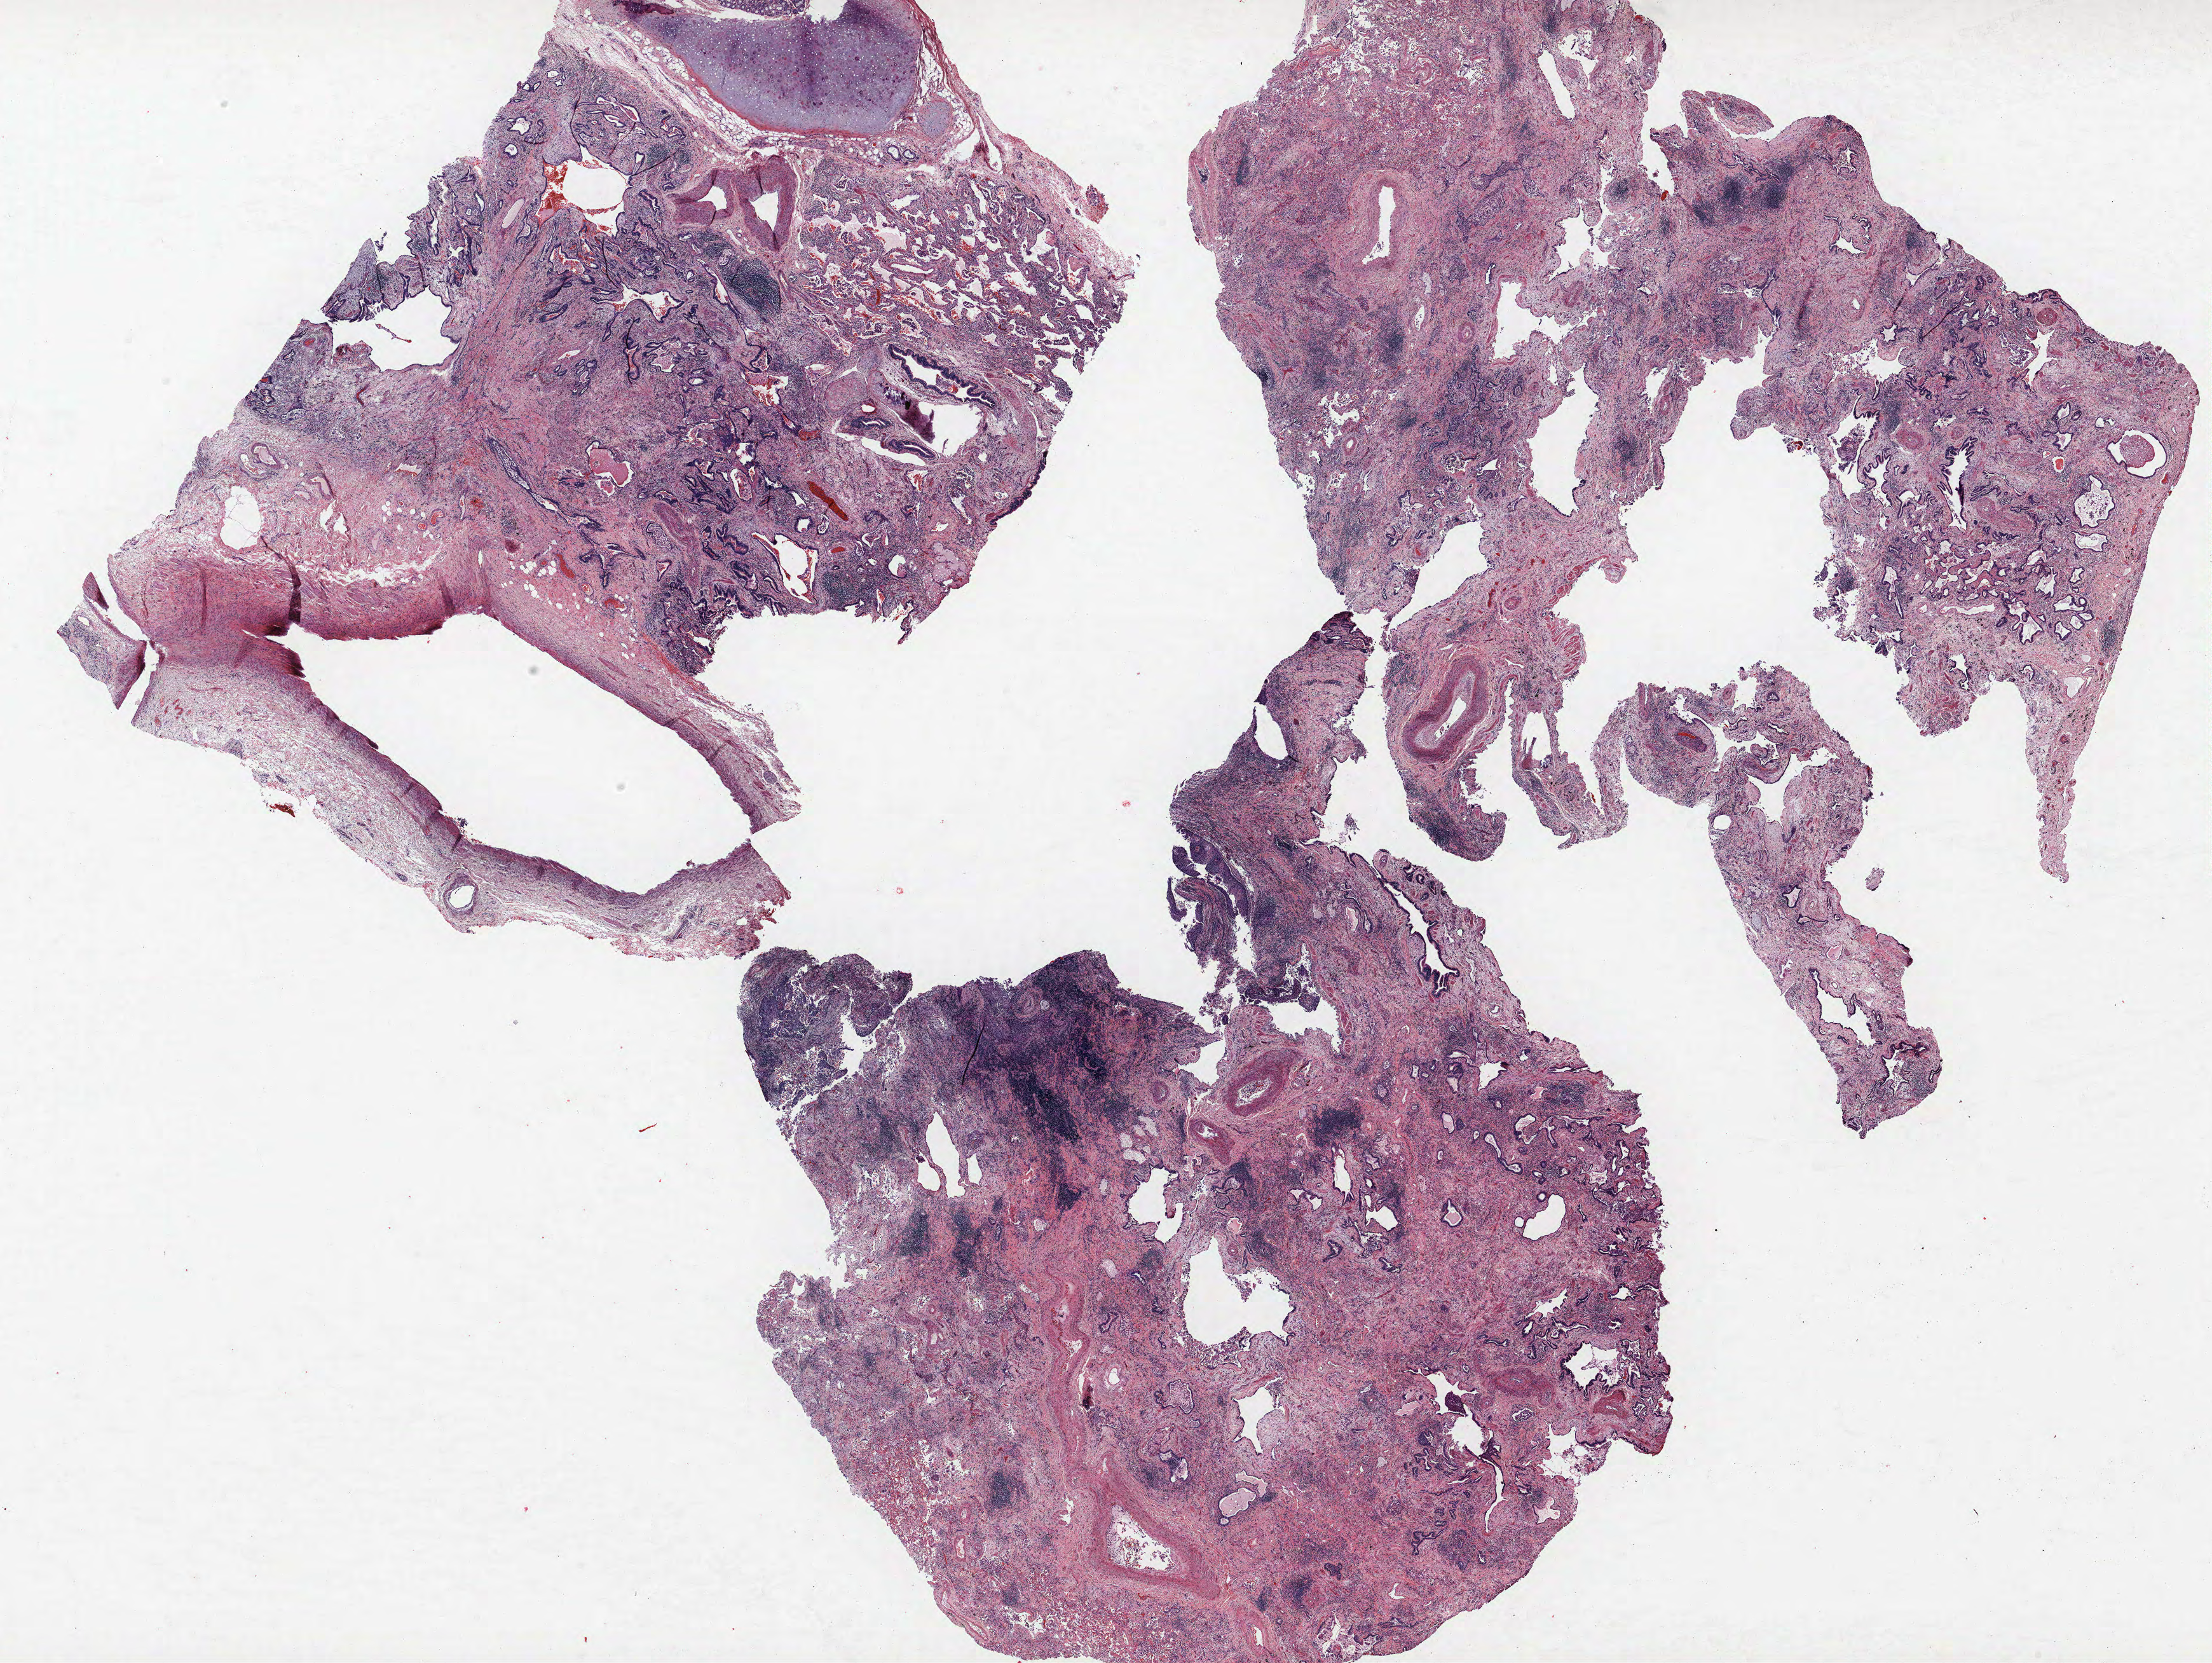
Whole-slide histology image, H&E-stained, shown as a low-resolution overview of the whole scanned area (about 27.8 x 20.9 mm, from a 40x scan); FFPE section; lung tissue. Male, age 68 at enrolment. Grade: well differentiated (G1).
* primary tumour location (clinical record): left upper lobe
* tumour size (pathology): 17 mm
* stage (AJCC 6th edition): IA
* participant's lung-cancer diagnosis: Squamous cell carcinoma, NOS